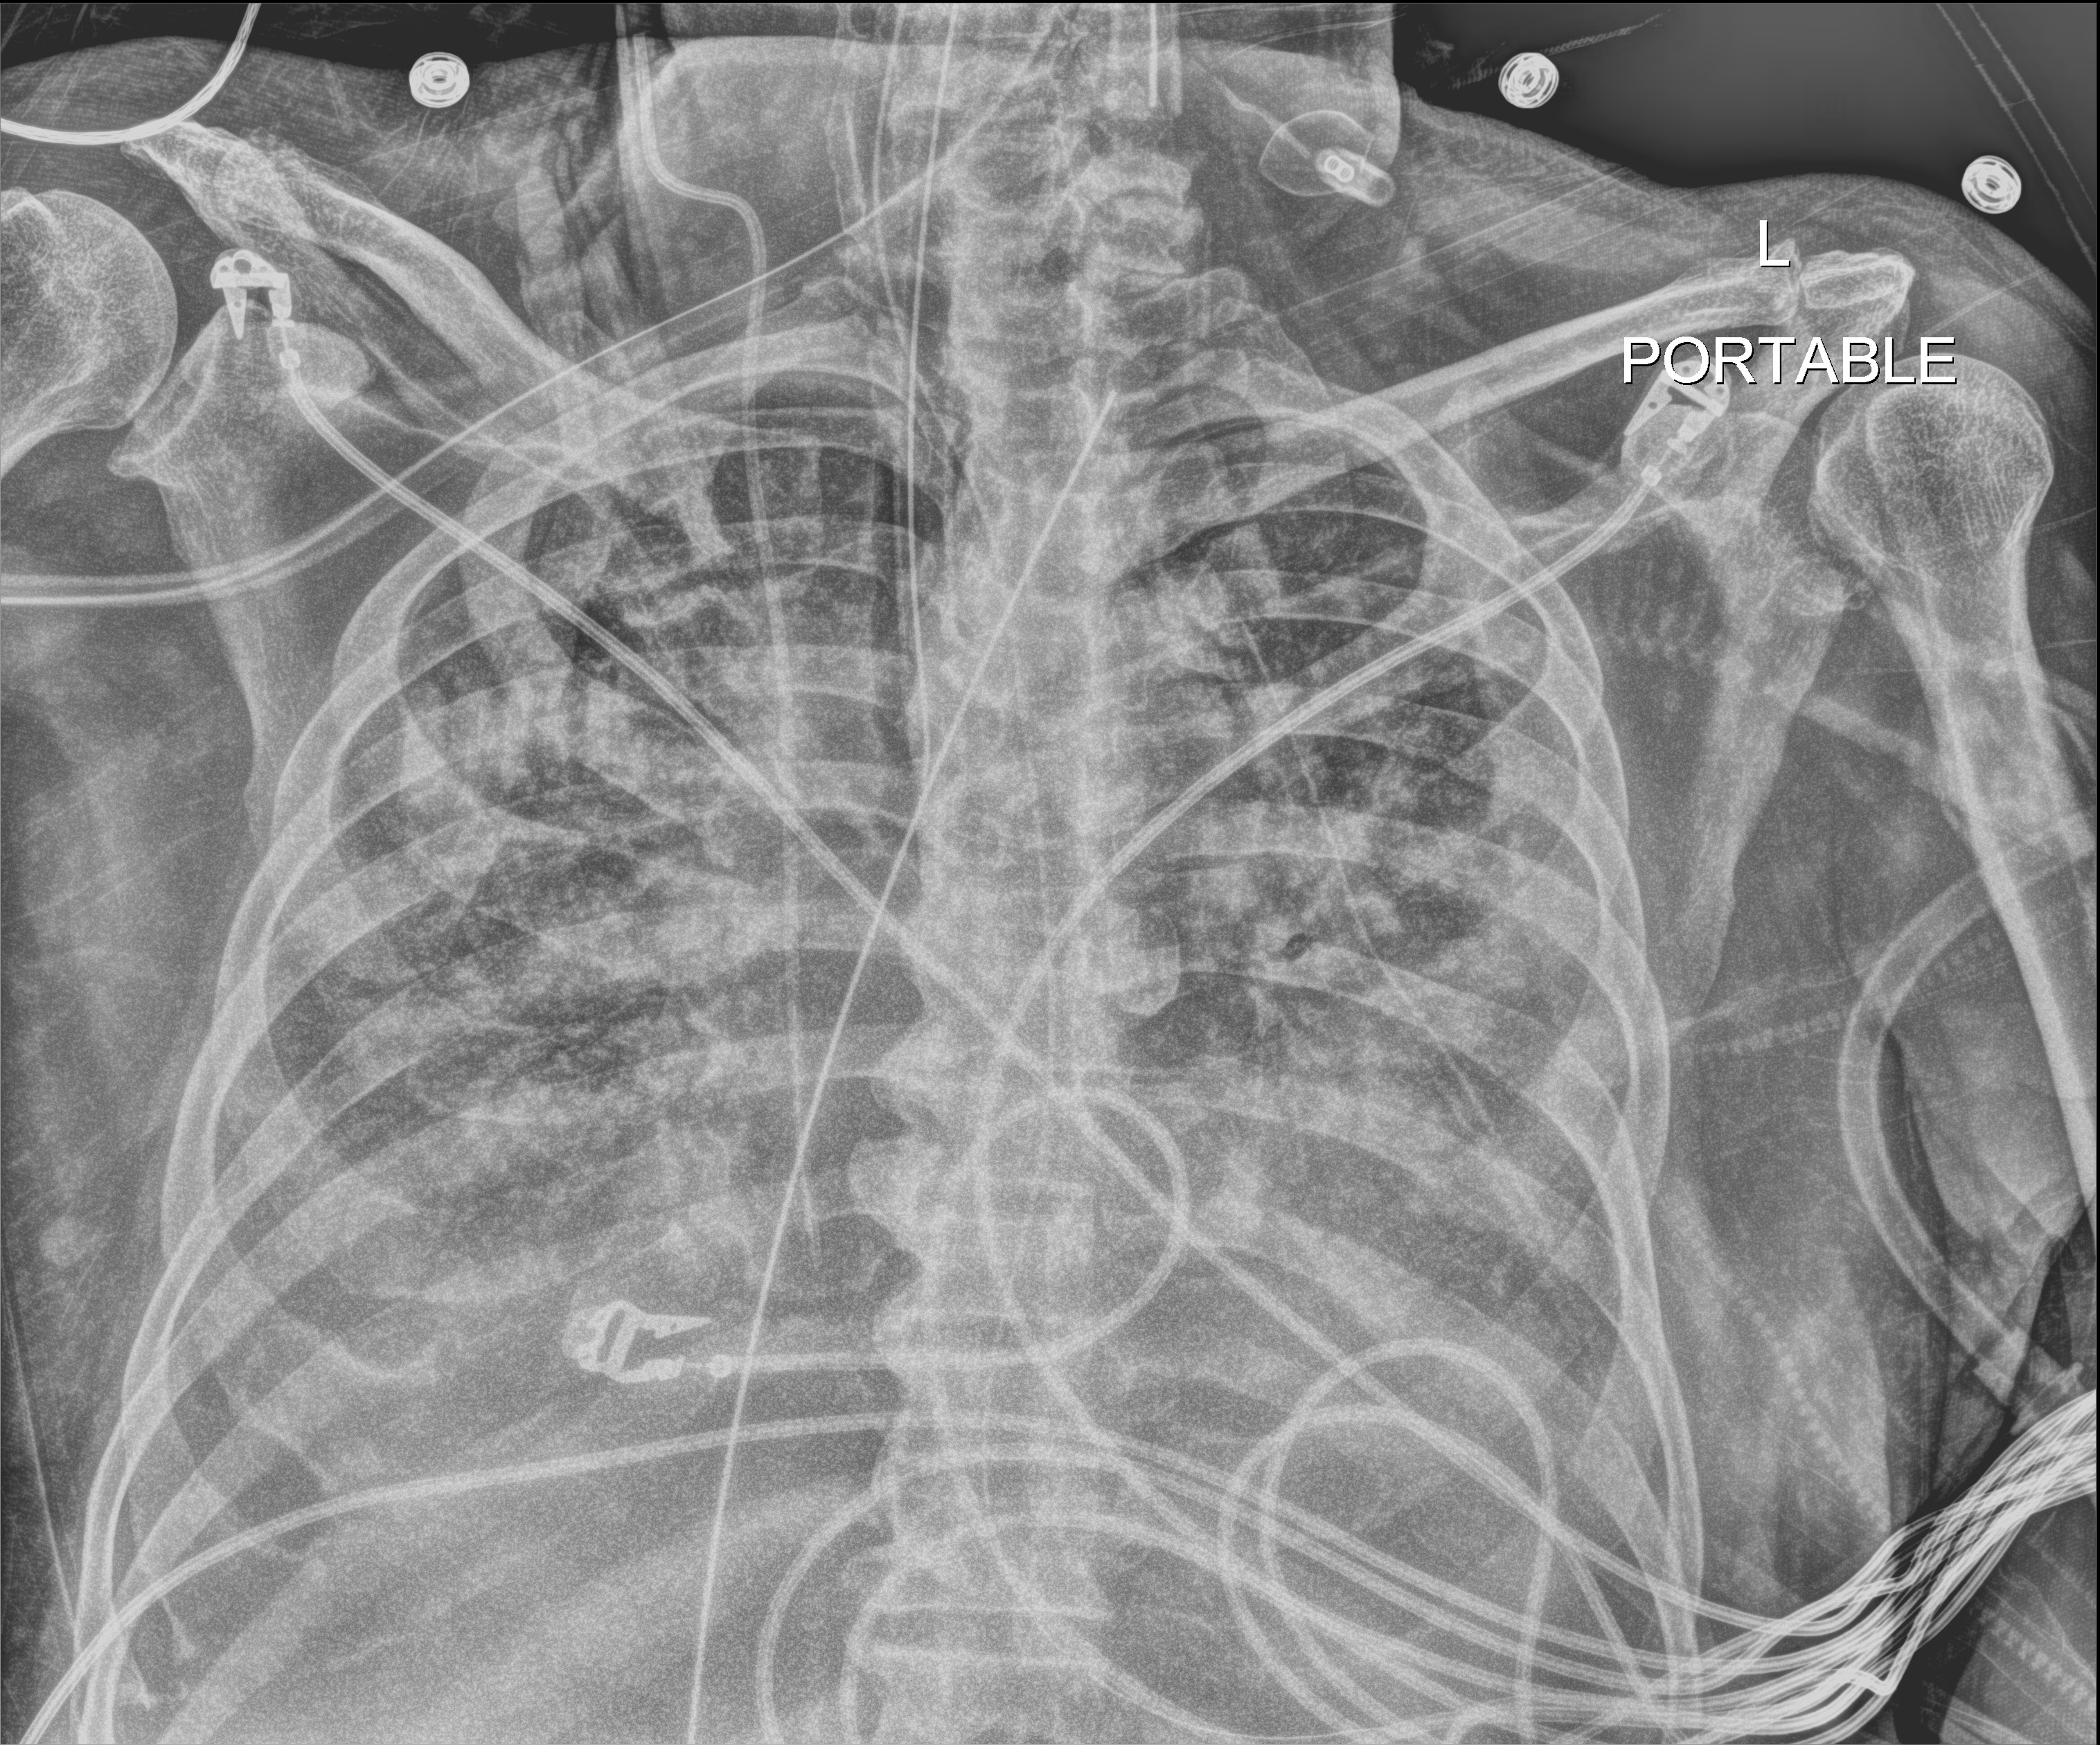
Portable chest radiograph; anteroposterior (AP) projection. Male patient hospitalised with COVID-19, age 75–90 years.
From the hospital-stay record, not from the radiograph (when in the stay this image was taken is not recorded): diabetes (admission record): no; admitted to intensive care during this hospital stay: yes; mechanically ventilated during this hospital stay: yes.